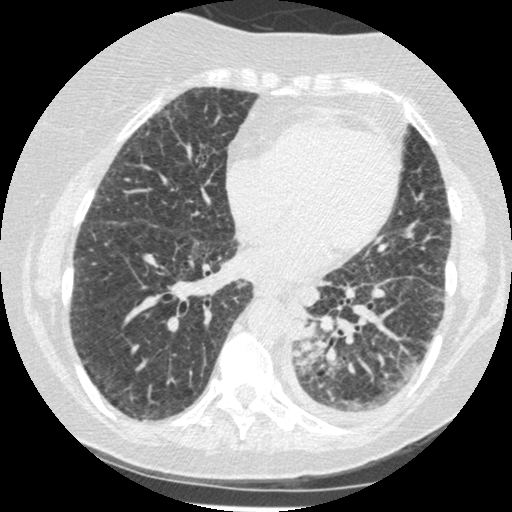
Low-dose screening chest CT, one axial slice. Position 79 of 341 along the scan axis. Reconstruction kernel STANDARD. 120 kVp. Lung window (W 1500 / L -600 HU). 512 × 512 image matrix, field of view 310 × 310 mm.
Structures marked on this image (expert manual segmentation):
- lesion 1 (tumor, lower lobe of left lung): bounding box [x1, y1, x2, y2] px = [294, 323, 316, 342]